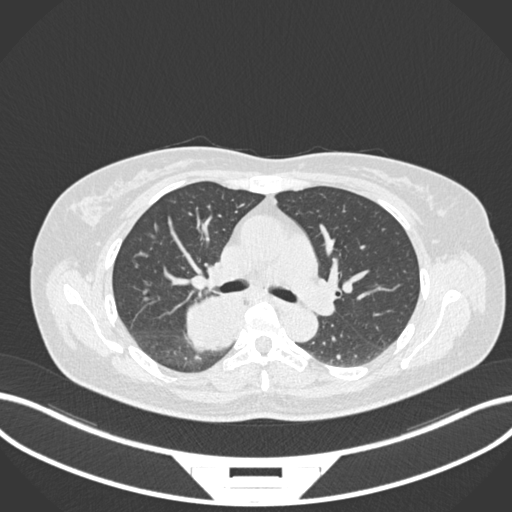
Chest CT, one axial slice. Position 615 of 677 along the scan axis. Reconstruction kernel B30f. 120 kVp. Lung window (W 1500 / L -600 HU). 1 mm slice thickness. 512 × 512 image matrix. Patient: female, 54 years. From the clinical record (not read from this slice): clinical TNM (as recorded): T4 N0 M0.
Structures marked on this image (rectangle marked by the reading radiologist):
- lung tumour (recorded histology: adenocarcinoma): bounding box <181,292,253,352> (left, top, right, bottom; pixels)